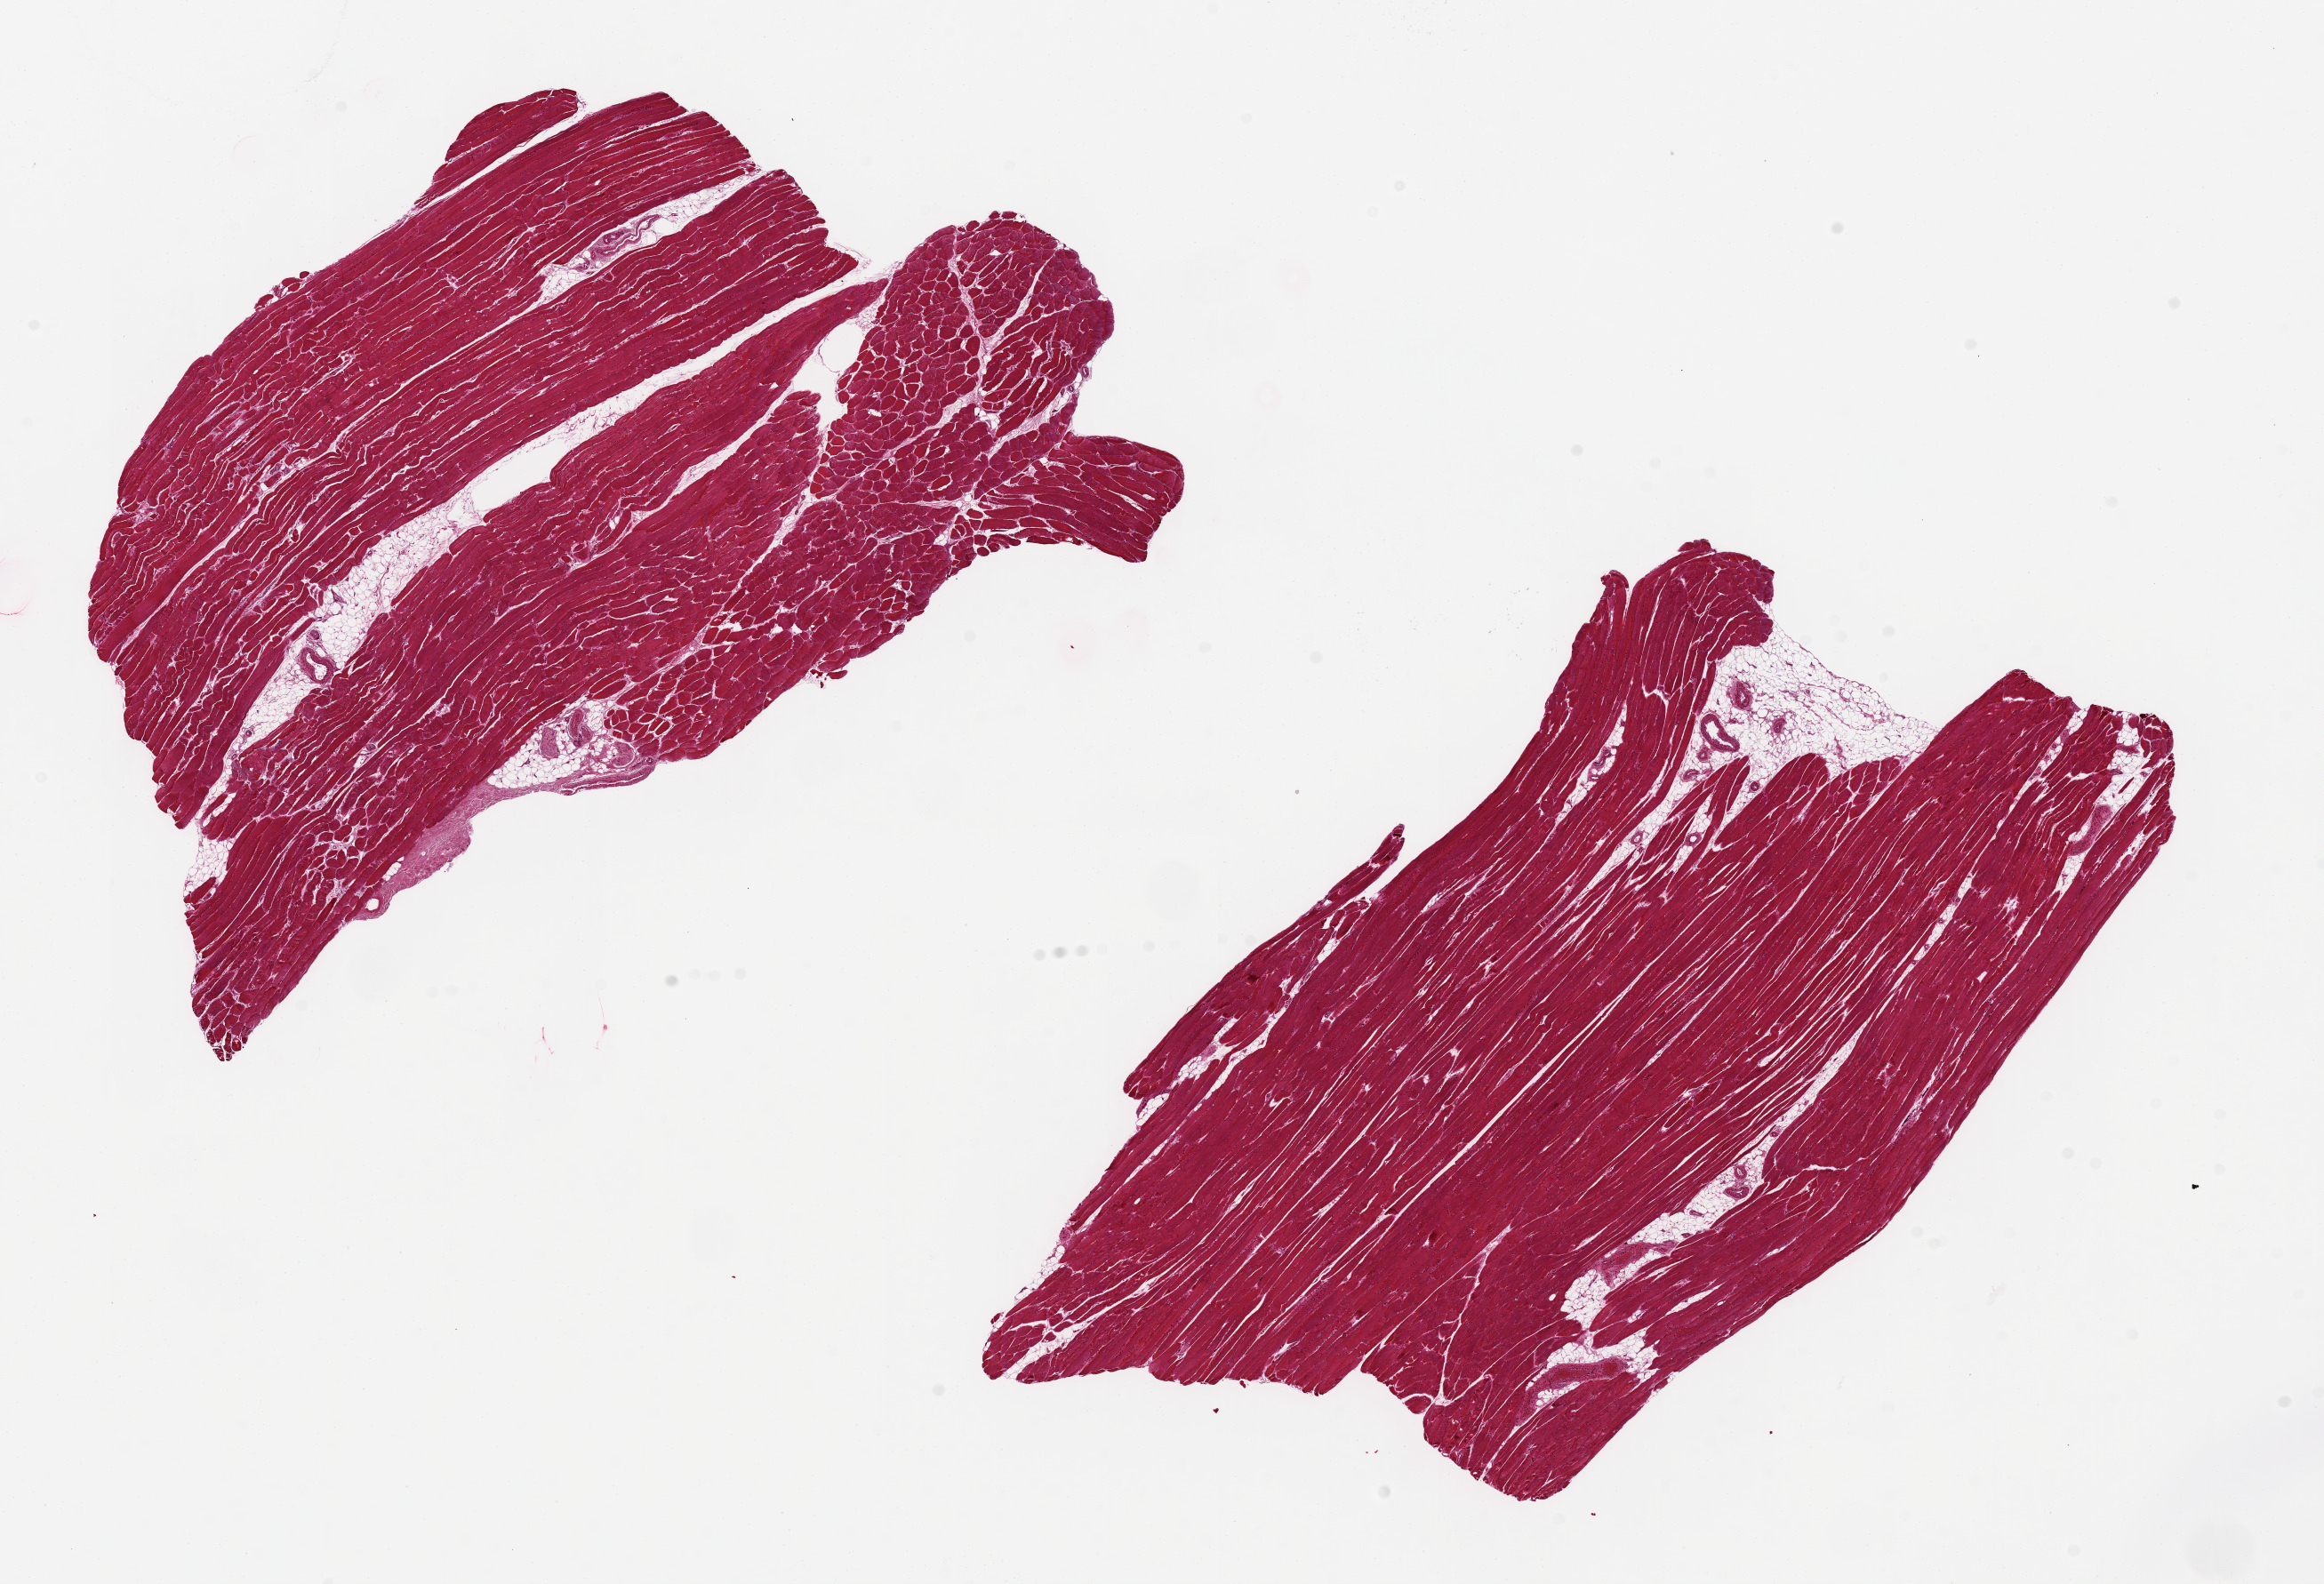
Haematoxylin and eosin whole-slide image, brightfield, low-resolution overview of the scanned area, about 20.7 x 14.1 mm (acquisition: 20x scan). PAXgene-fixed paraffin-embedded (PFPE) section. Sampled site (target tissue): skeletal muscle. Donor tissue sample. Male donor.
Review note (as recorded): 2 pieces, 10x7 & 10x6mm; well trimmed, <10% internal adipose.